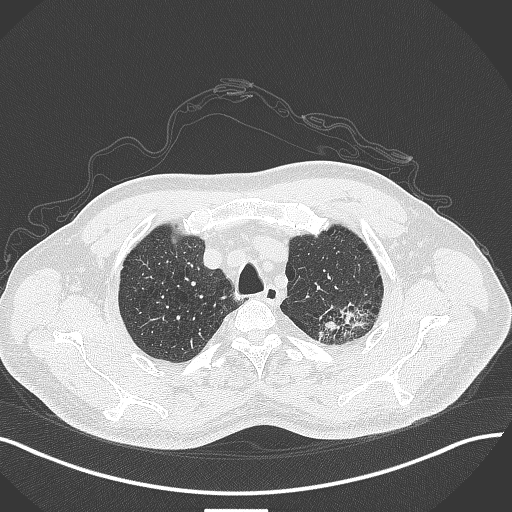
Chest CT, one axial slice. Slice 357 of 429 in the series (ordered by position). Reconstruction kernel B70f. 120 kVp. Lung window (W 1500 / L -600 HU). 512 × 512 image matrix, field of view 400 × 400 mm. Male patient, age 55 years. From the clinical record (not read from this slice): clinical TNM (as recorded): T3 N0 M1c; histopathological grade: G3.
Annotated regions visible in this slice (bounding box drawn by a radiologist):
- lung tumour (recorded histology: adenocarcinoma): bounding box (x1, y1, x2, y2) in pixels: (311, 299, 377, 344)